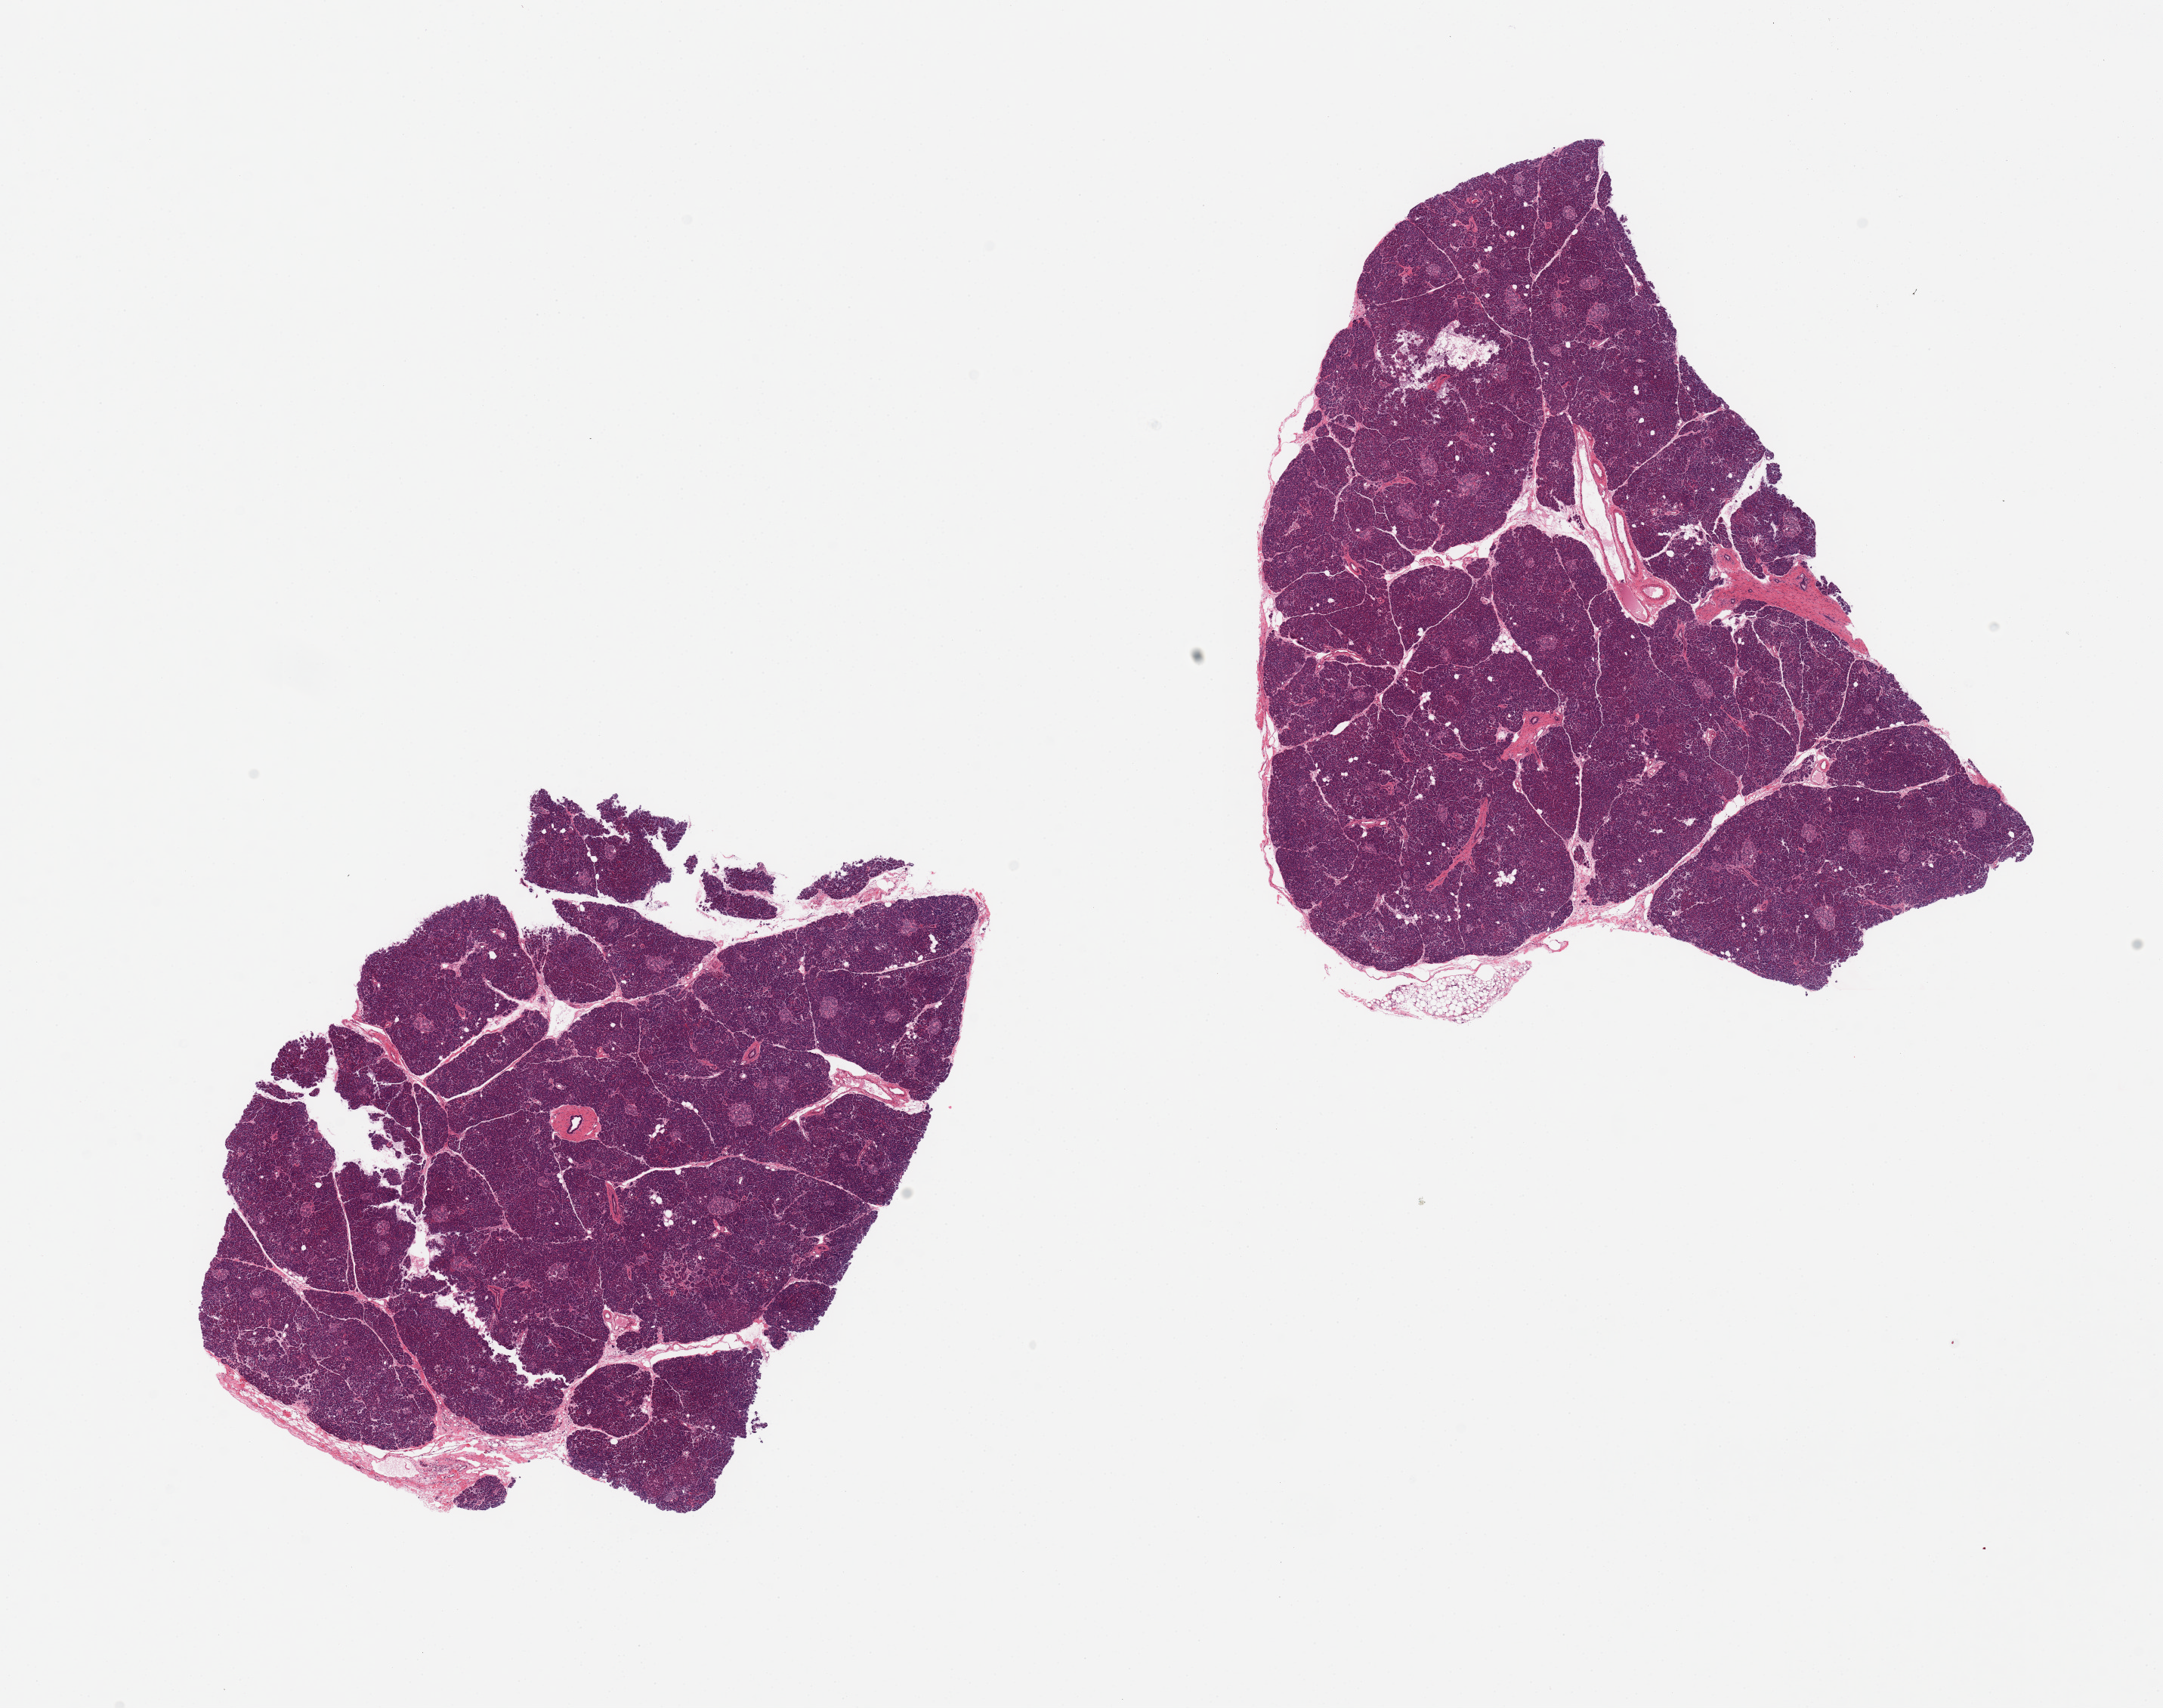
Digitized hematoxylin and eosin (H&E)-stained section, brightfield, low-resolution overview of the scanned area, about 22.6 x 17.9 mm (acquisition: 20x scan), PAXgene-fixed, paraffin-embedded tissue, sampled site (target tissue): pancreas, donor tissue sample.
Reviewer comment on this tissue sample: 2 pieces; well dissected, no fat.